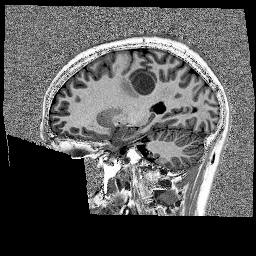
Brain MRI from a brain-tumour surgery series, one sagittal slice. Position 68 of 176 along the scan axis. 1 mm slice thickness. 256 × 256 image matrix. From the clinical record (not read from this slice): histopathology: Glioblastoma; WHO grade: 4; IDH mutation: no.
Outlined on this slice (expert manual segmentation):
- tumour: bounding box [x1, y1, x2, y2] px = [118, 62, 175, 90]